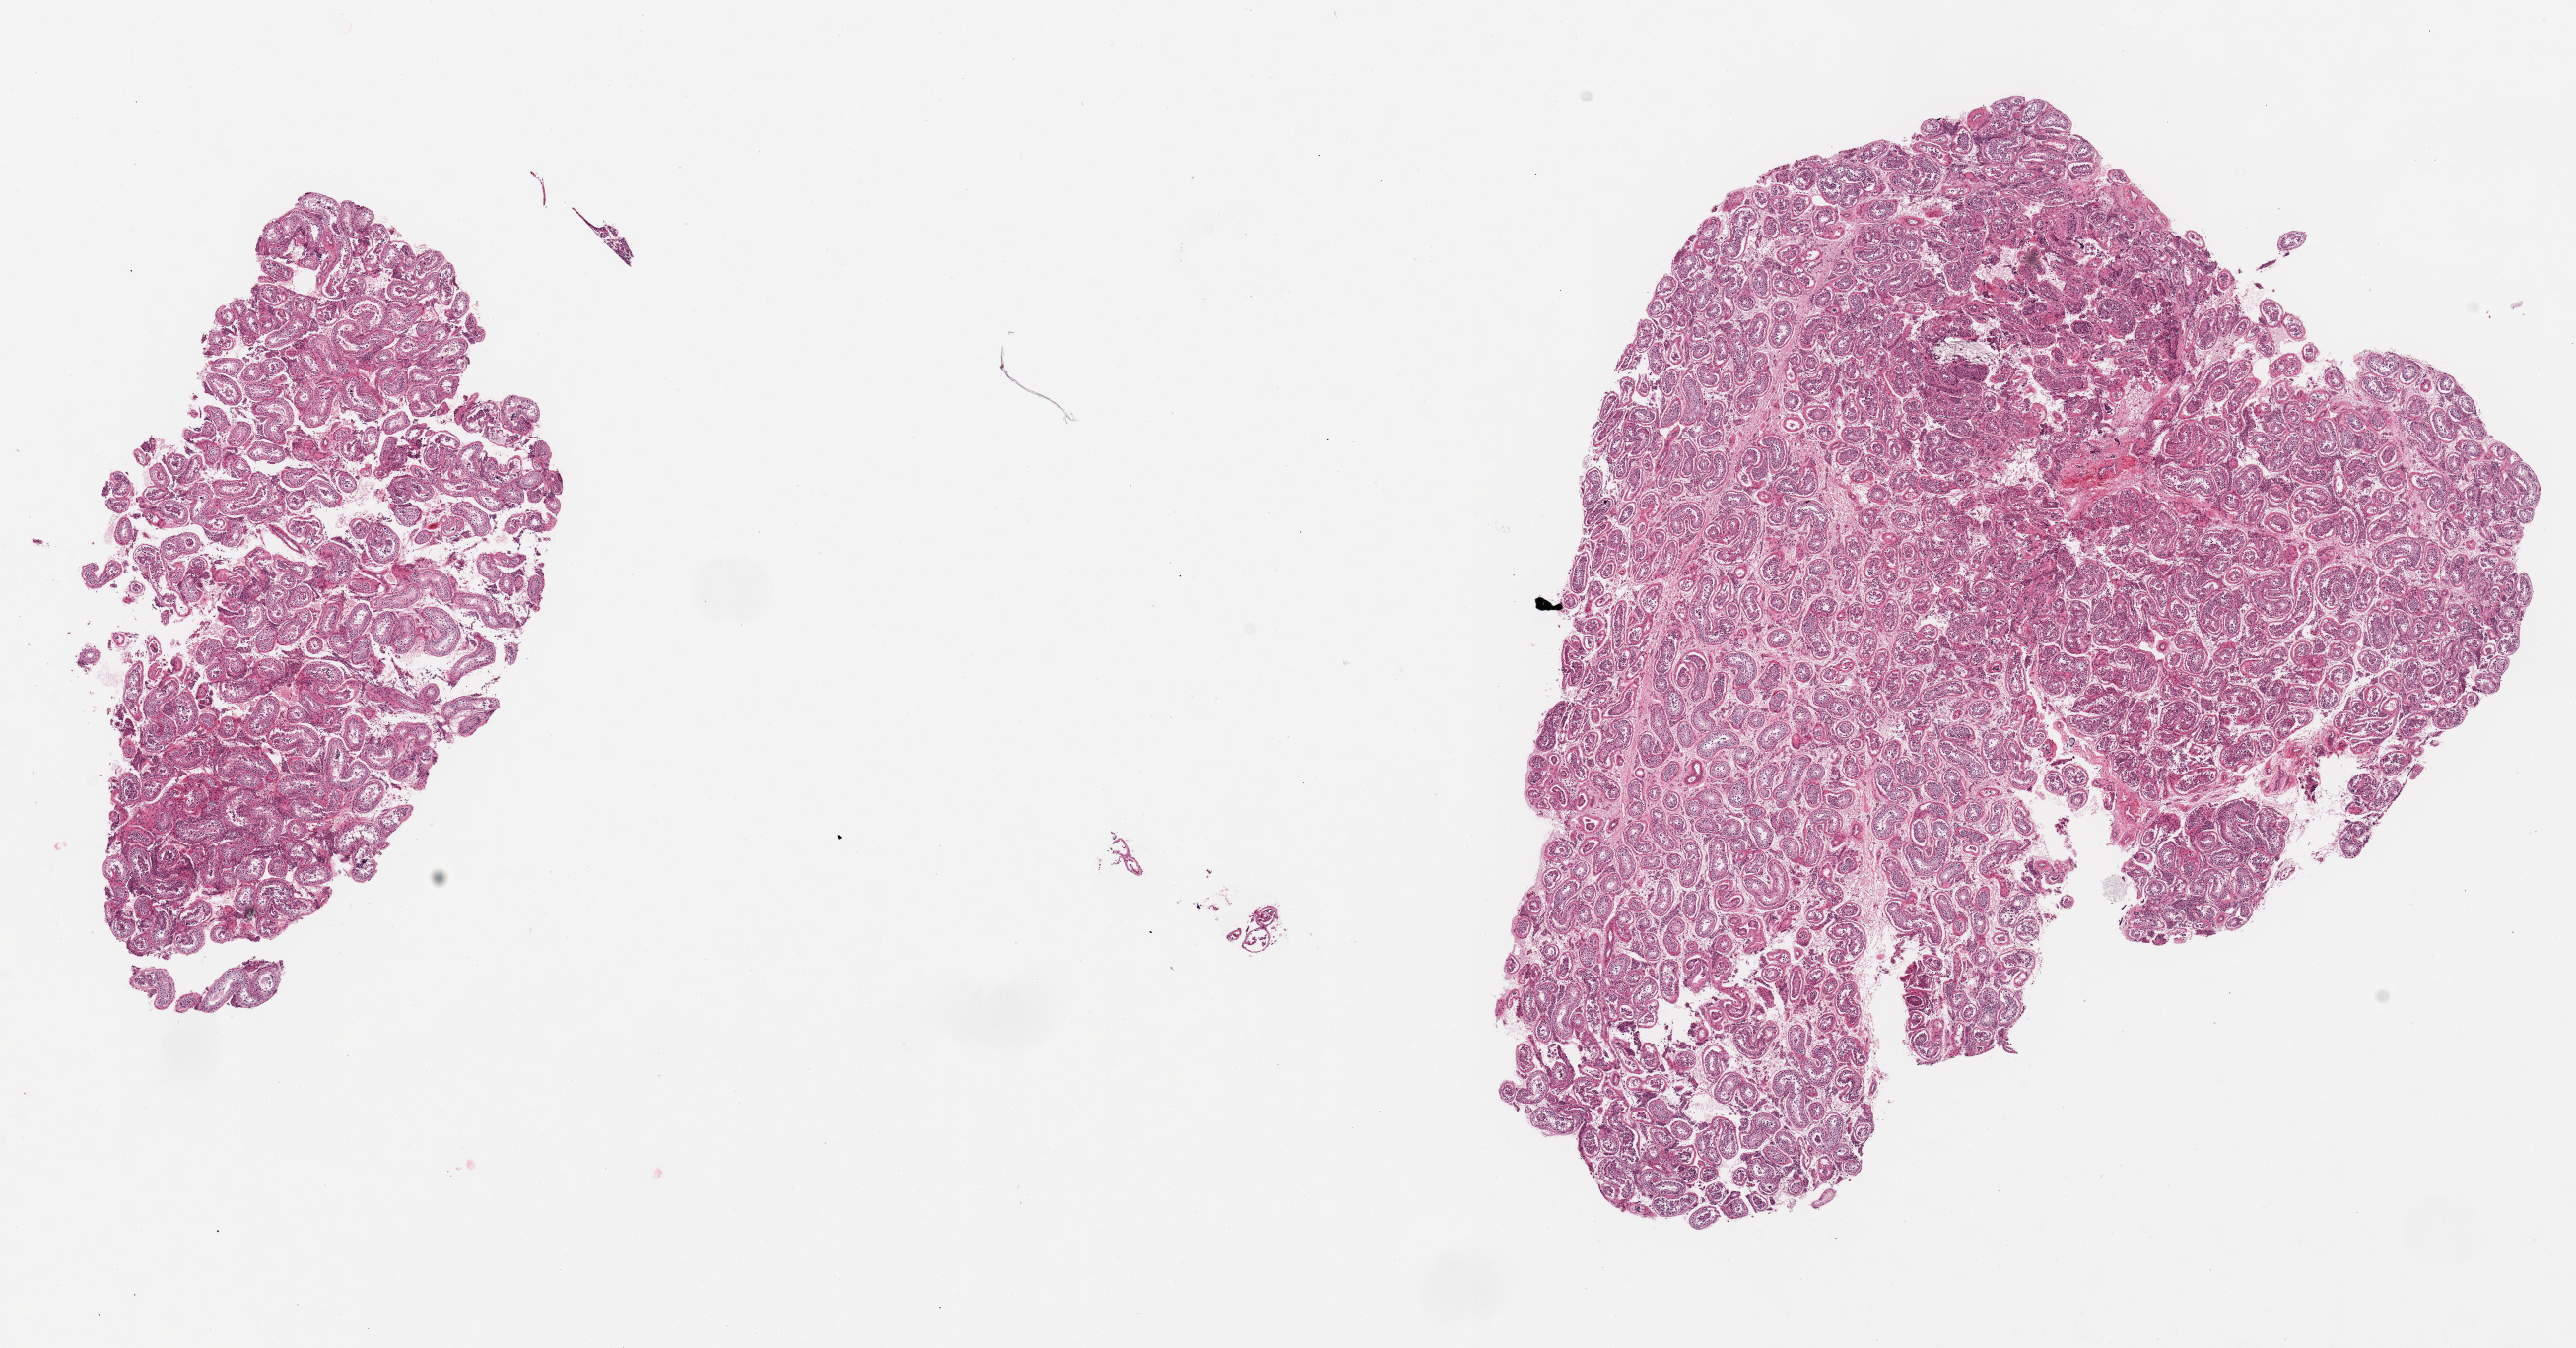
Haematoxylin and eosin whole-slide image — low-resolution overview of the scanned area, about 20.7 x 10.8 mm (slide scanned at 20x), PAXgene-fixed, paraffin-embedded tissue, sampled site (target tissue): testis, donor tissue sample. Donor: male.
- pathologist's review note for this sample: 2 pieces; active spermatogenesis